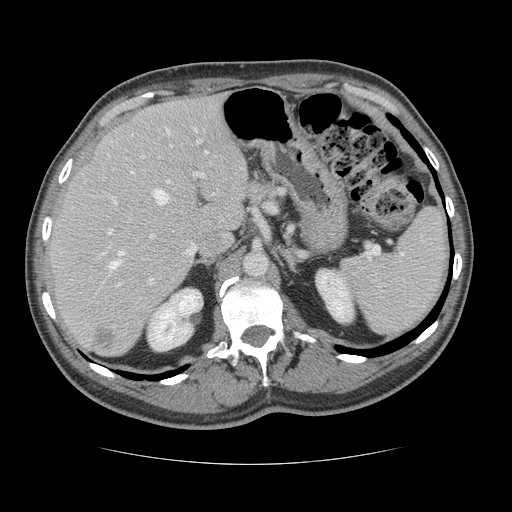
Contrast-enhanced abdominal CT, one axial slice. Position 86 of 134 along the scan axis. 120 kVp. Soft-tissue window (W 400 / L 40 HU). 2.5 mm slice thickness. 512 × 512 image matrix, field of view 377 × 377 mm. Male patient, age 68 years. From the clinical record (not read from this slice): diagnosis: colorectal cancer liver metastases, imaged before liver resection; multiple liver metastases: yes; largest metastasis: 2.2 cm; disease in both lobes: no.
Annotated regions visible in this slice (outlined manually by an expert reader):
- hepatic veins: box from (x=109, y=129) to (x=213, y=269) px
- liver: (x=50, y=97)–(x=249, y=356)
- planned liver remnant (the part of the liver to remain after resection): (x=50, y=97)–(x=249, y=337)
- portal vein (with intrahepatic branches): (x=108, y=128)–(x=206, y=284)
- liver metastasis: (x=93, y=328)–(x=116, y=349)